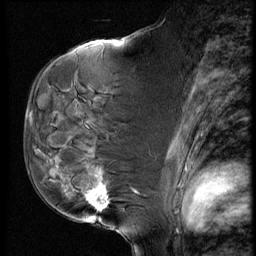
Breast MRI (dynamic contrast-enhanced), one sagittal slice; slice 34 of 60 in the series (ordered by position); dynamic contrast-enhanced series, image 2 of 4 at this slice position (ordered by acquisition); 1.5 T; TE 4.2 ms, TR 9 ms; 2.5 mm slice thickness; 256 × 256 image matrix, field of view 180 × 180 mm. Patient: female, 50 years. Case-level facts recorded for this patient, not image findings: setting: breast cancer imaged before/during neoadjuvant chemotherapy; receptor status: HR-positive, HER2-negative.
Annotated regions visible in this slice (semi-automatic segmentation, software-assisted and operator-edited):
- analysis volume of interest (the breast-tissue region the enhancement analysis was run in; not a lesion): bounding box <48,109,135,230> (left, top, right, bottom; pixels)
- tumour enhancement mask (voxels above the 140 % enhancement threshold inside the analysis volume of interest): <86,189,109,210>